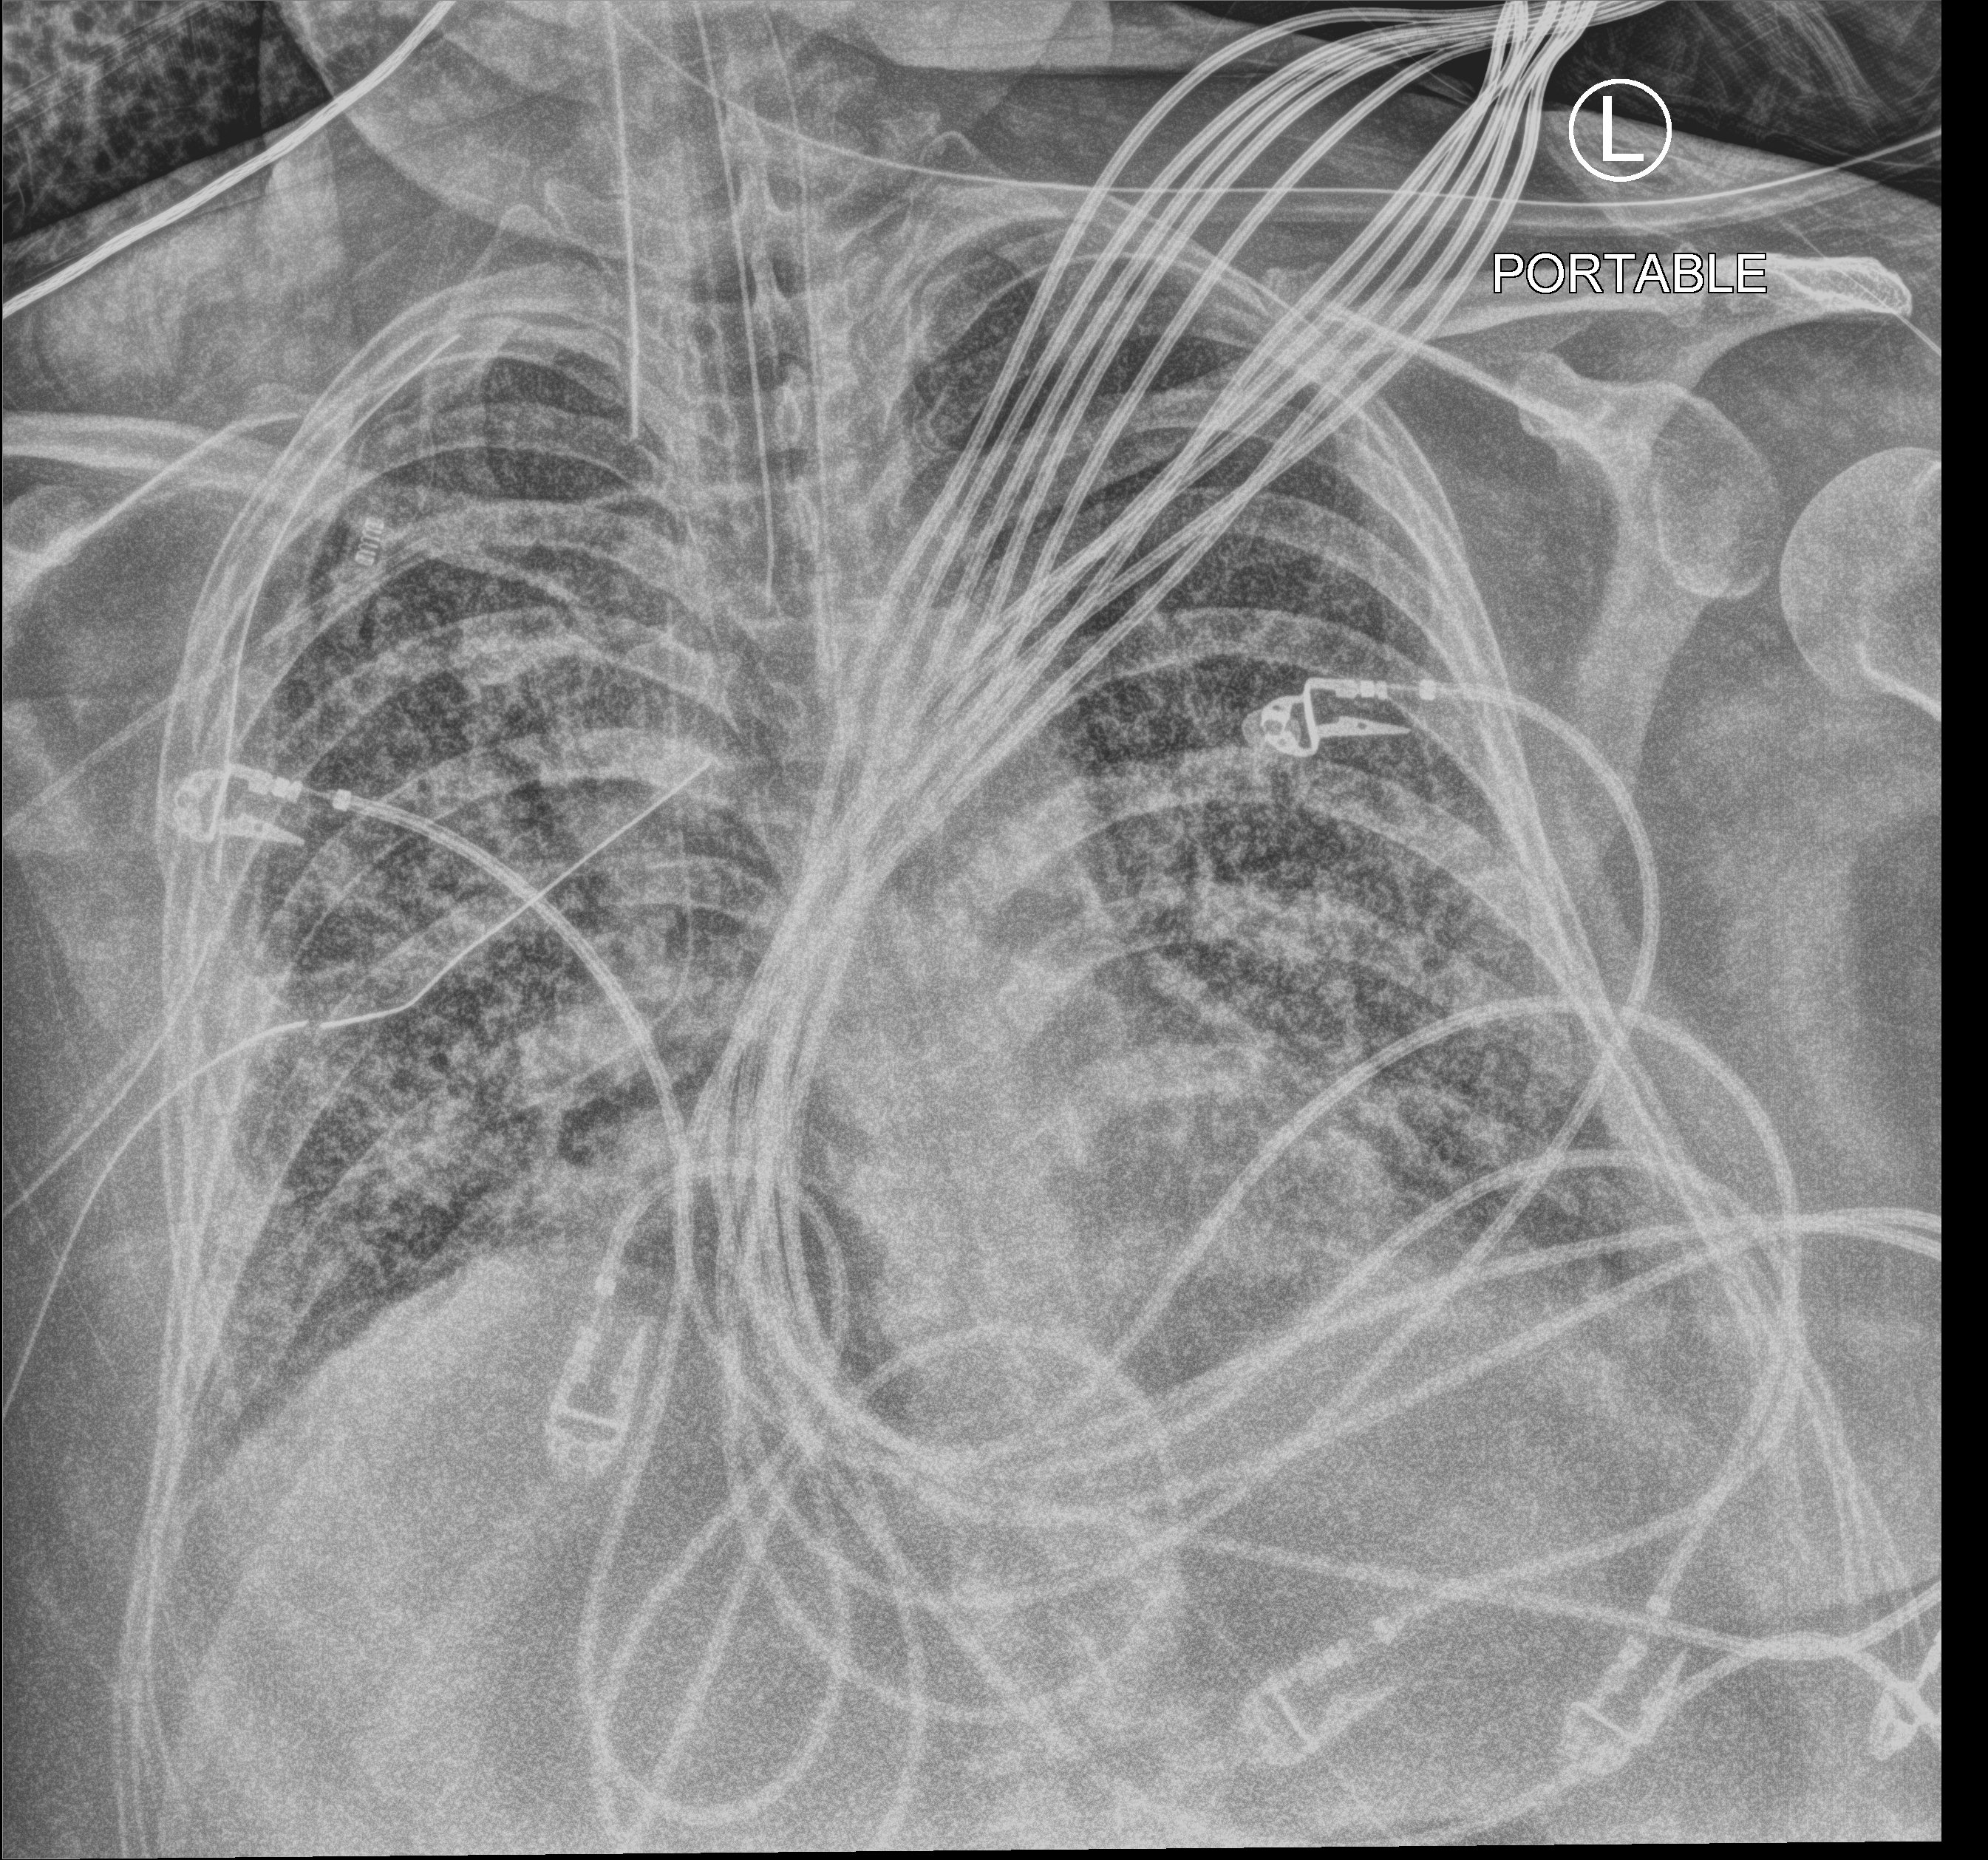
Bedside chest radiograph (computed radiography), anteroposterior (AP) projection. Patient hospitalised with COVID-19, aged 18–59 years.
Admission-level facts for this patient (not findings on this image; timing relative to this image not recorded): chronic kidney disease (admission record): no.